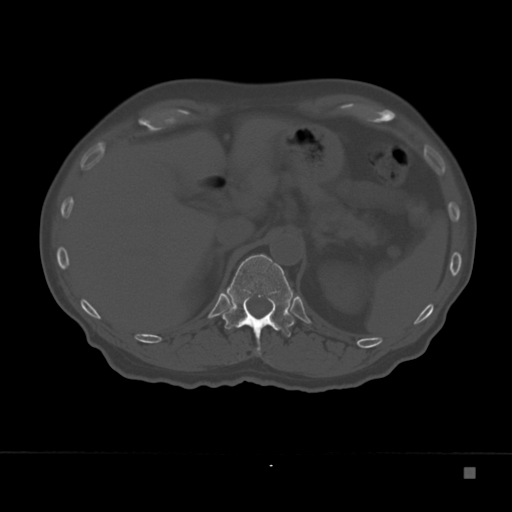
CT including the spine, one axial slice; position 134 of 332 along the scan axis; reconstruction kernel Br40s; bone window (W 1800 / L 400 HU); 1.5 mm slice thickness; 512 × 512 image matrix. Patient: male, 72 years. From the clinical record (not read from this slice): primary cancer: skeletal.
Structures marked on this image (semi-automatically segmented with operator editing):
- T12 vertebra: bounding box [x1, y1, x2, y2] px = [223, 254, 295, 354]